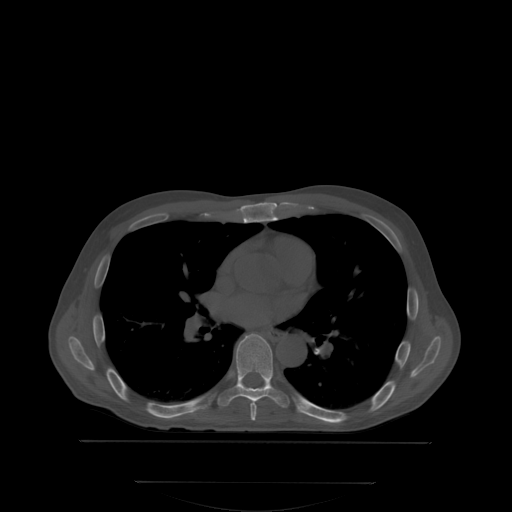
CT including the spine, one axial slice. Slice 227 of 350 in the series (ordered by position). Bone window (W 1800 / L 400 HU). 2.5 mm slice thickness. 512 × 512 image matrix, field of view 500 × 500 mm. Patient: male, 58 years. From the clinical record (not read from this slice): primary cancer: prostate; vertebrae with lytic lesions (as recorded): L1.
Structures marked on this image (semi-automatically segmented with operator editing):
- T6 vertebra: bounding box [x1, y1, x2, y2] px = [250, 403, 257, 420]
- T7 vertebra: [217, 333, 290, 408]